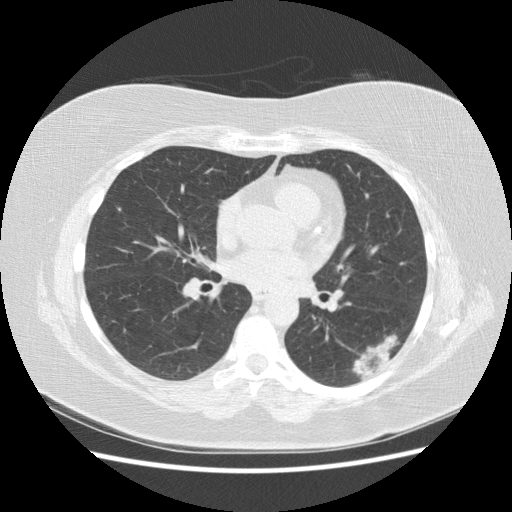
Low-dose screening chest CT, one axial slice. Slice 78 of 151 in the series (ordered by position). Lung window (W 1500 / L -600 HU). 2.5 mm slice thickness. 512 × 512 image matrix, field of view 360 × 360 mm.
Structures marked on this image (outlined manually by an expert reader):
- lesion 1 (tumor, lower lobe of left lung): bounding box (x1, y1, x2, y2) in pixels: (352, 334, 400, 379)